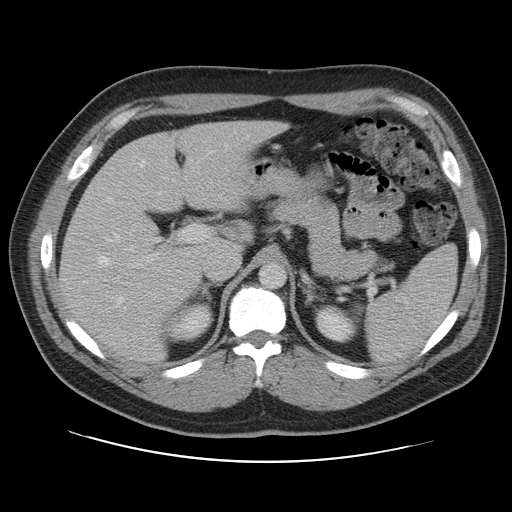
Contrast-enhanced abdominal CT, one axial slice. Position 72 of 109 along the scan axis. Intravenous contrast given. Soft-tissue window (W 400 / L 40 HU). 5 mm slice thickness. 512 × 512 image matrix, field of view 402 × 402 mm. Male patient, age 35 years. From the clinical record (not read from this slice): diagnosis: colorectal cancer liver metastases, imaged before liver resection; multiple liver metastases: yes; largest metastasis: 2.8 cm; chemotherapy before resection: yes.
Annotated regions visible in this slice (expert manual segmentation):
- hepatic veins: bounding box [x1, y1, x2, y2] px = [97, 144, 228, 308]
- liver: [61, 121, 282, 361]
- planned liver remnant (the part of the liver to remain after resection): [61, 121, 280, 361]
- portal vein (with intrahepatic branches): [114, 160, 210, 299]